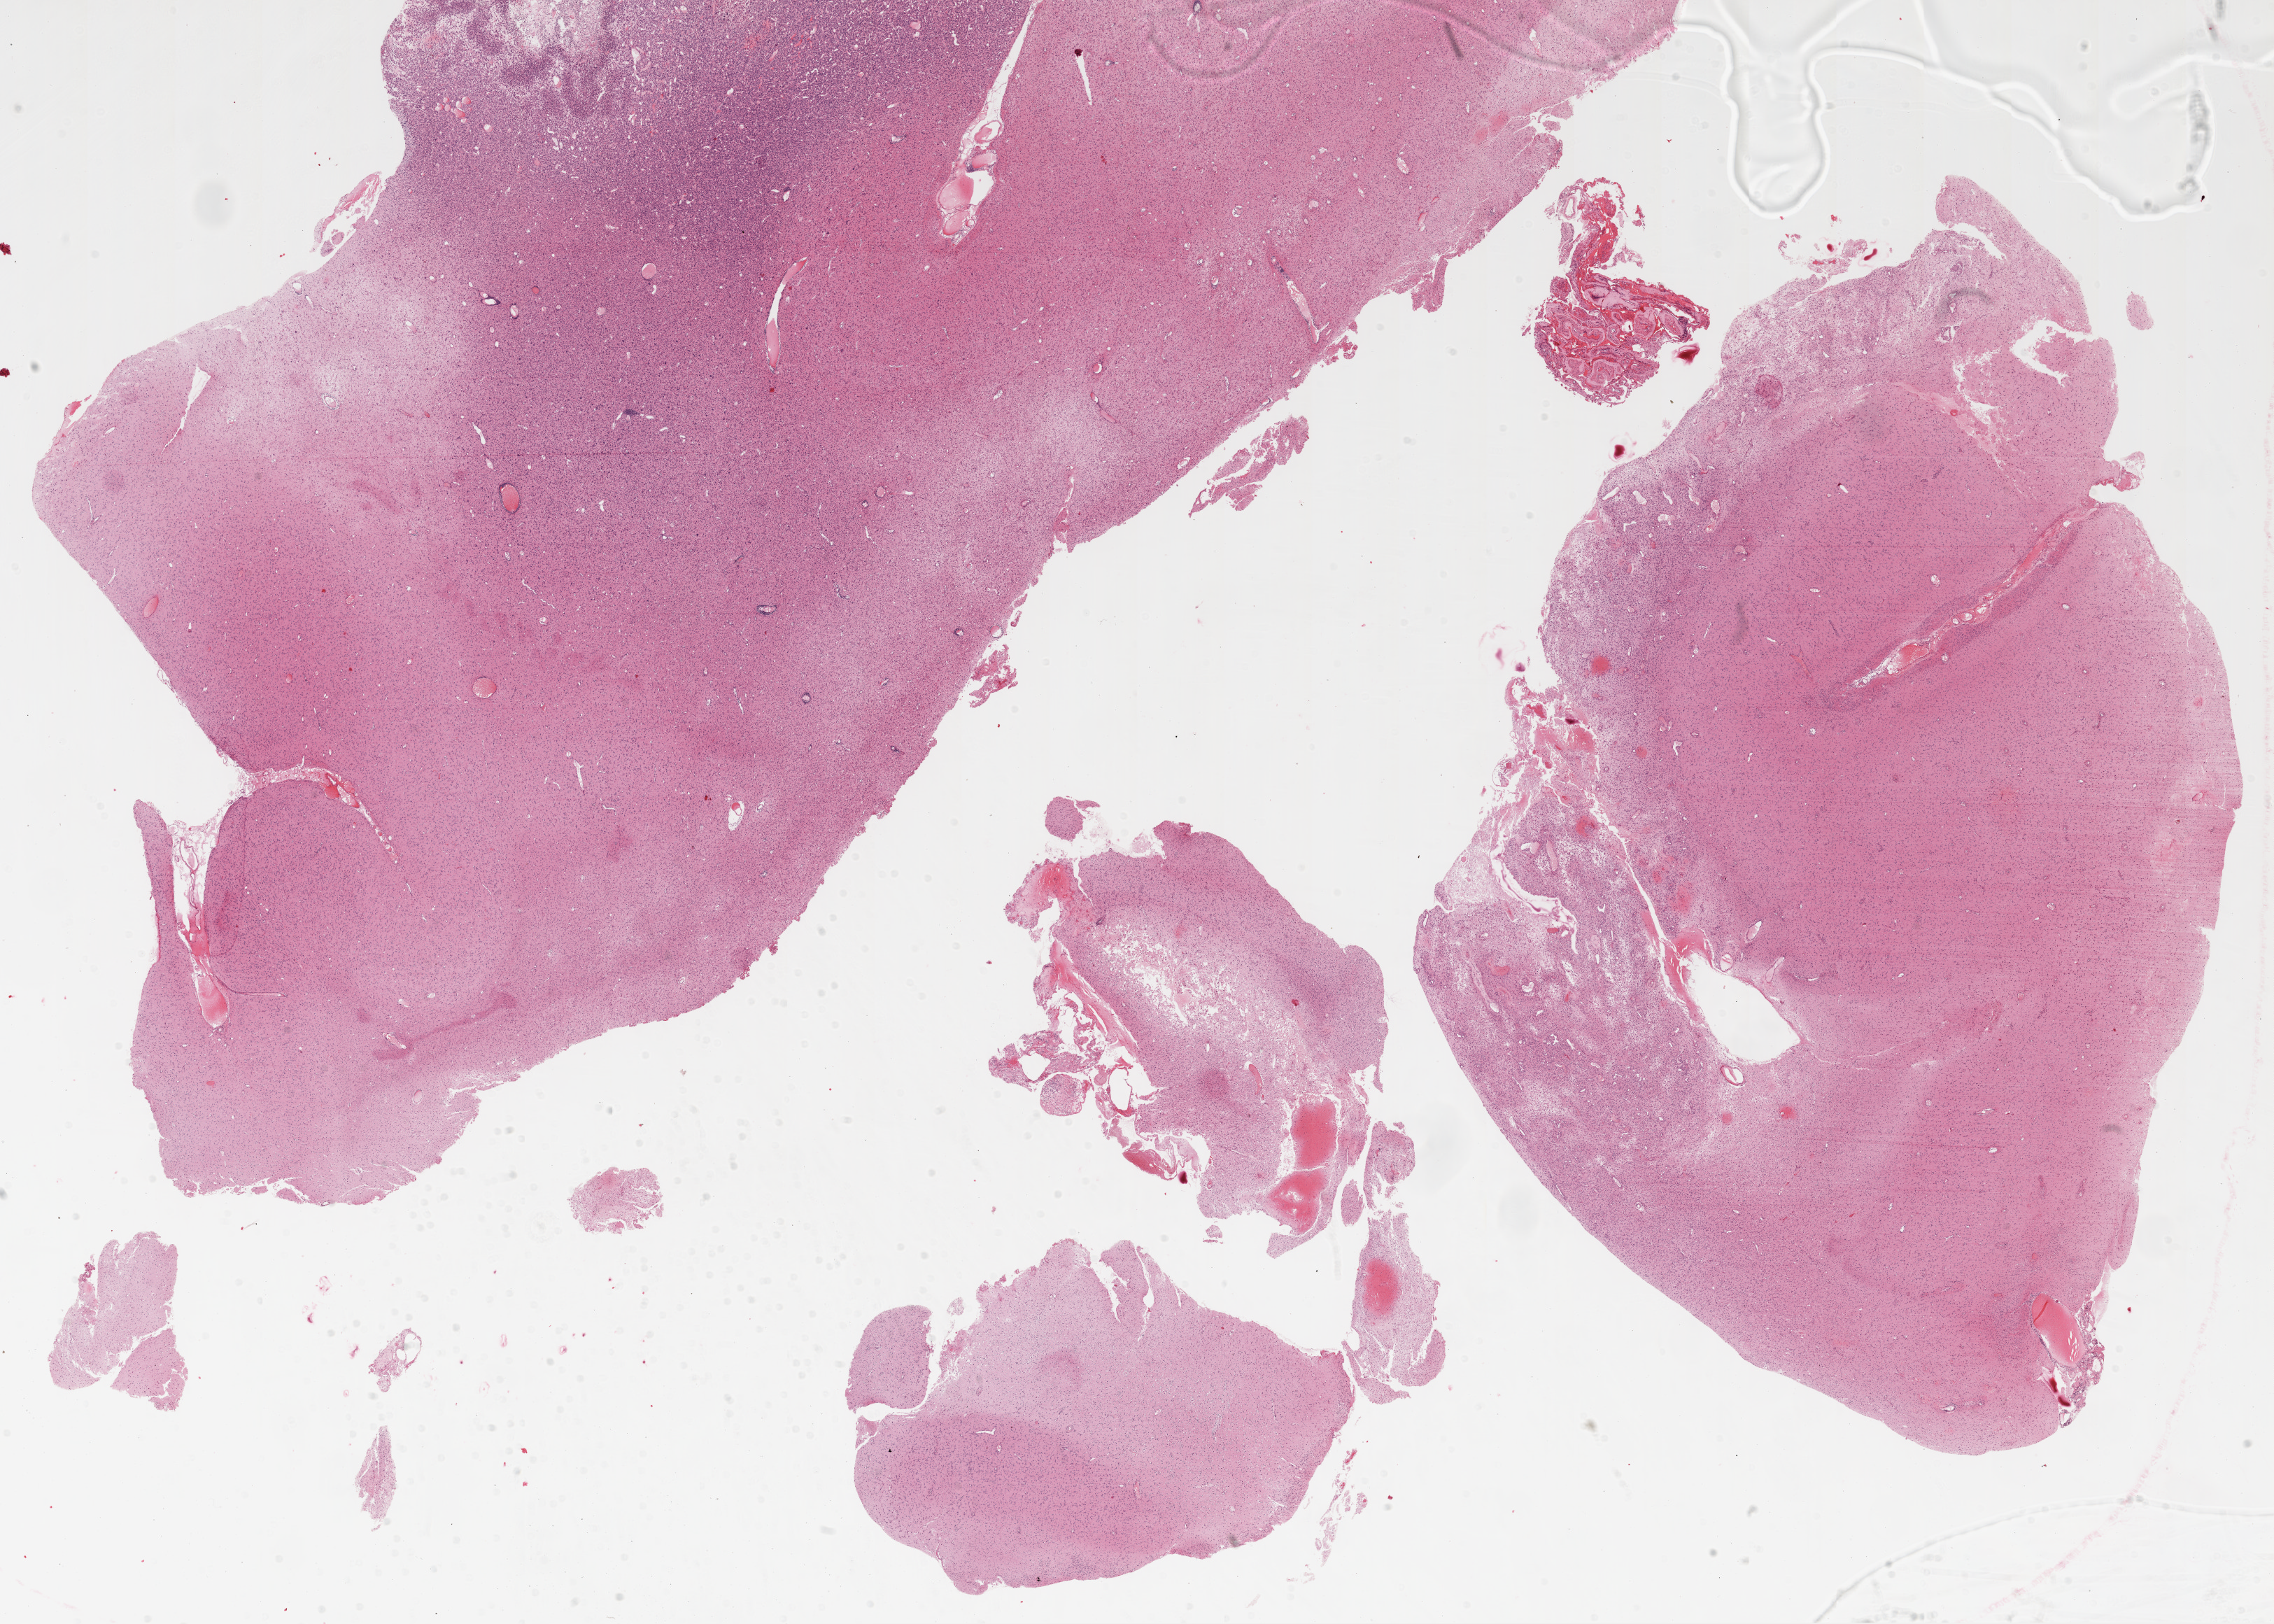
Hematoxylin and eosin (H&E) stained whole-slide image — whole scanned area (about 26.1 x 18.6 mm, slide scanned at 20x) shown as a low-resolution overview, formalin-fixed paraffin-embedded (FFPE) diagnostic section, sample: primary tumour, brain. Female, age 33 years at initial diagnosis.
Diagnosis: Glioblastoma.